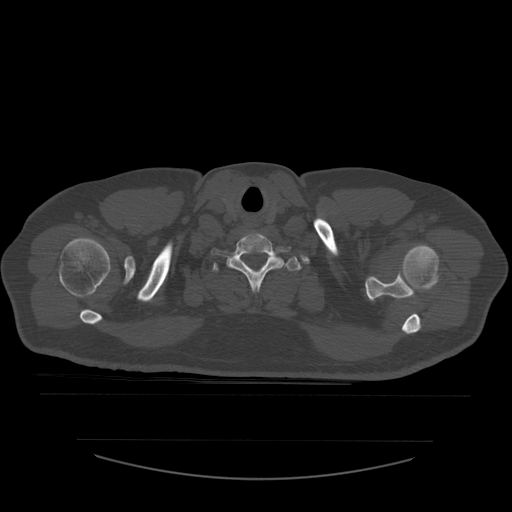
CT including the spine, one axial slice. Position 479 of 532 along the scan axis. Bone window (W 1800 / L 400 HU). 1.25 mm slice thickness. 512 × 512 image matrix. Patient age 44 years. From the clinical record (not read from this slice): primary cancer: soft tissue sarcoma.
Structures marked on this image (semi-automatic segmentation, software-assisted and operator-edited):
- T1 vertebra: bounding box [x1, y1, x2, y2] px = [213, 257, 302, 272]